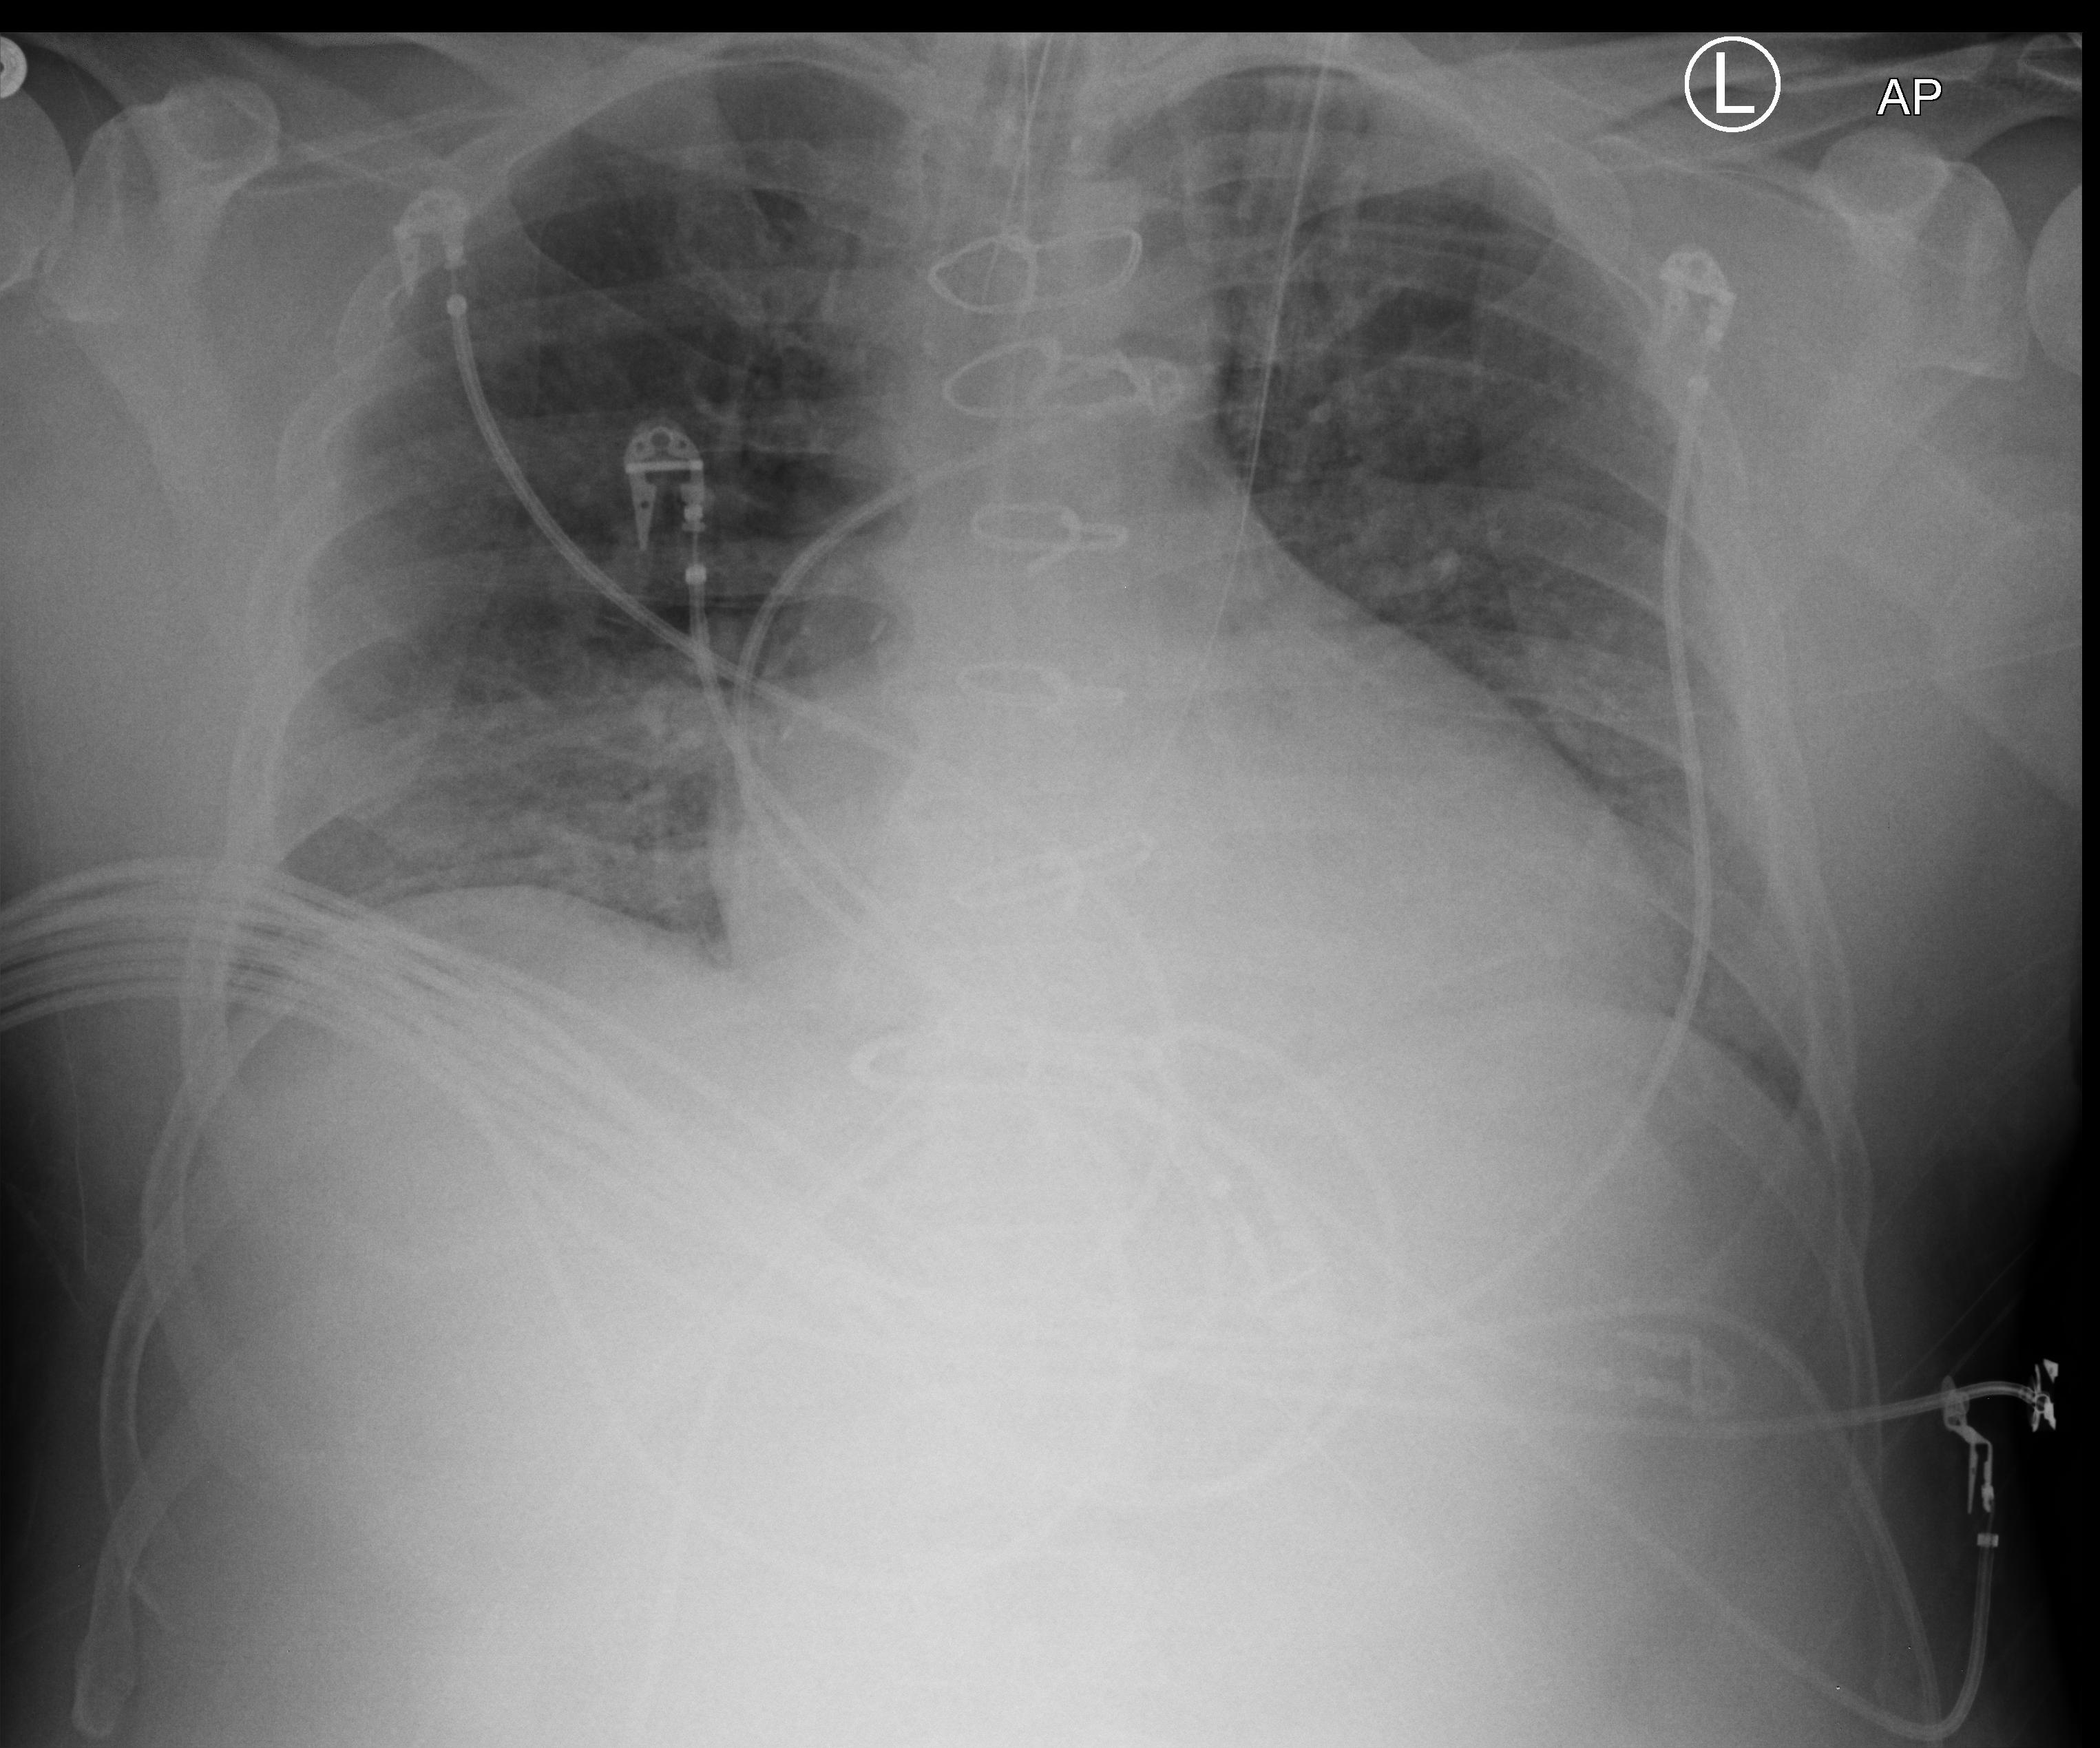
Bedside chest radiograph (computed radiography); anteroposterior (AP) projection. Patient hospitalised with COVID-19, aged 18–59 years.
Hospital-stay facts (about this admission, not read from this image; timing relative to this image not recorded): admitted to intensive care during this hospital stay: yes; length of hospital stay: 6 days.